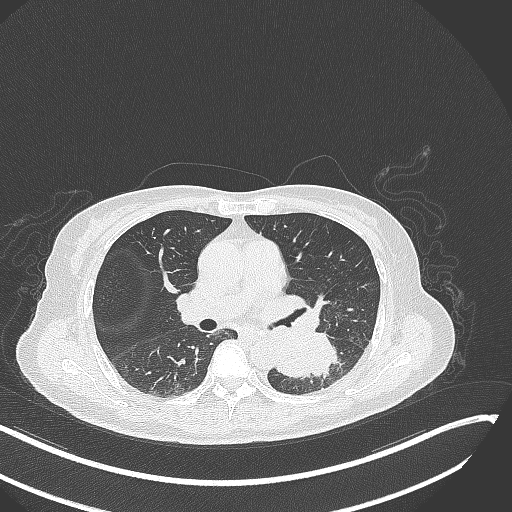
Chest CT, one axial slice. Position 156 of 342 along the scan axis. Reconstruction kernel B70f. Lung window (W 1500 / L -600 HU). 1 mm slice thickness. 512 × 512 image matrix. Patient: female, 64 years. Case-level facts recorded for this patient, not image findings: clinical TNM (as recorded): T3 N1 M1.
Outlined on this slice (rectangle marked by the reading radiologist):
- lung tumour (recorded histology: small cell carcinoma): bounding box (x1, y1, x2, y2) in pixels: (266, 325, 343, 380)